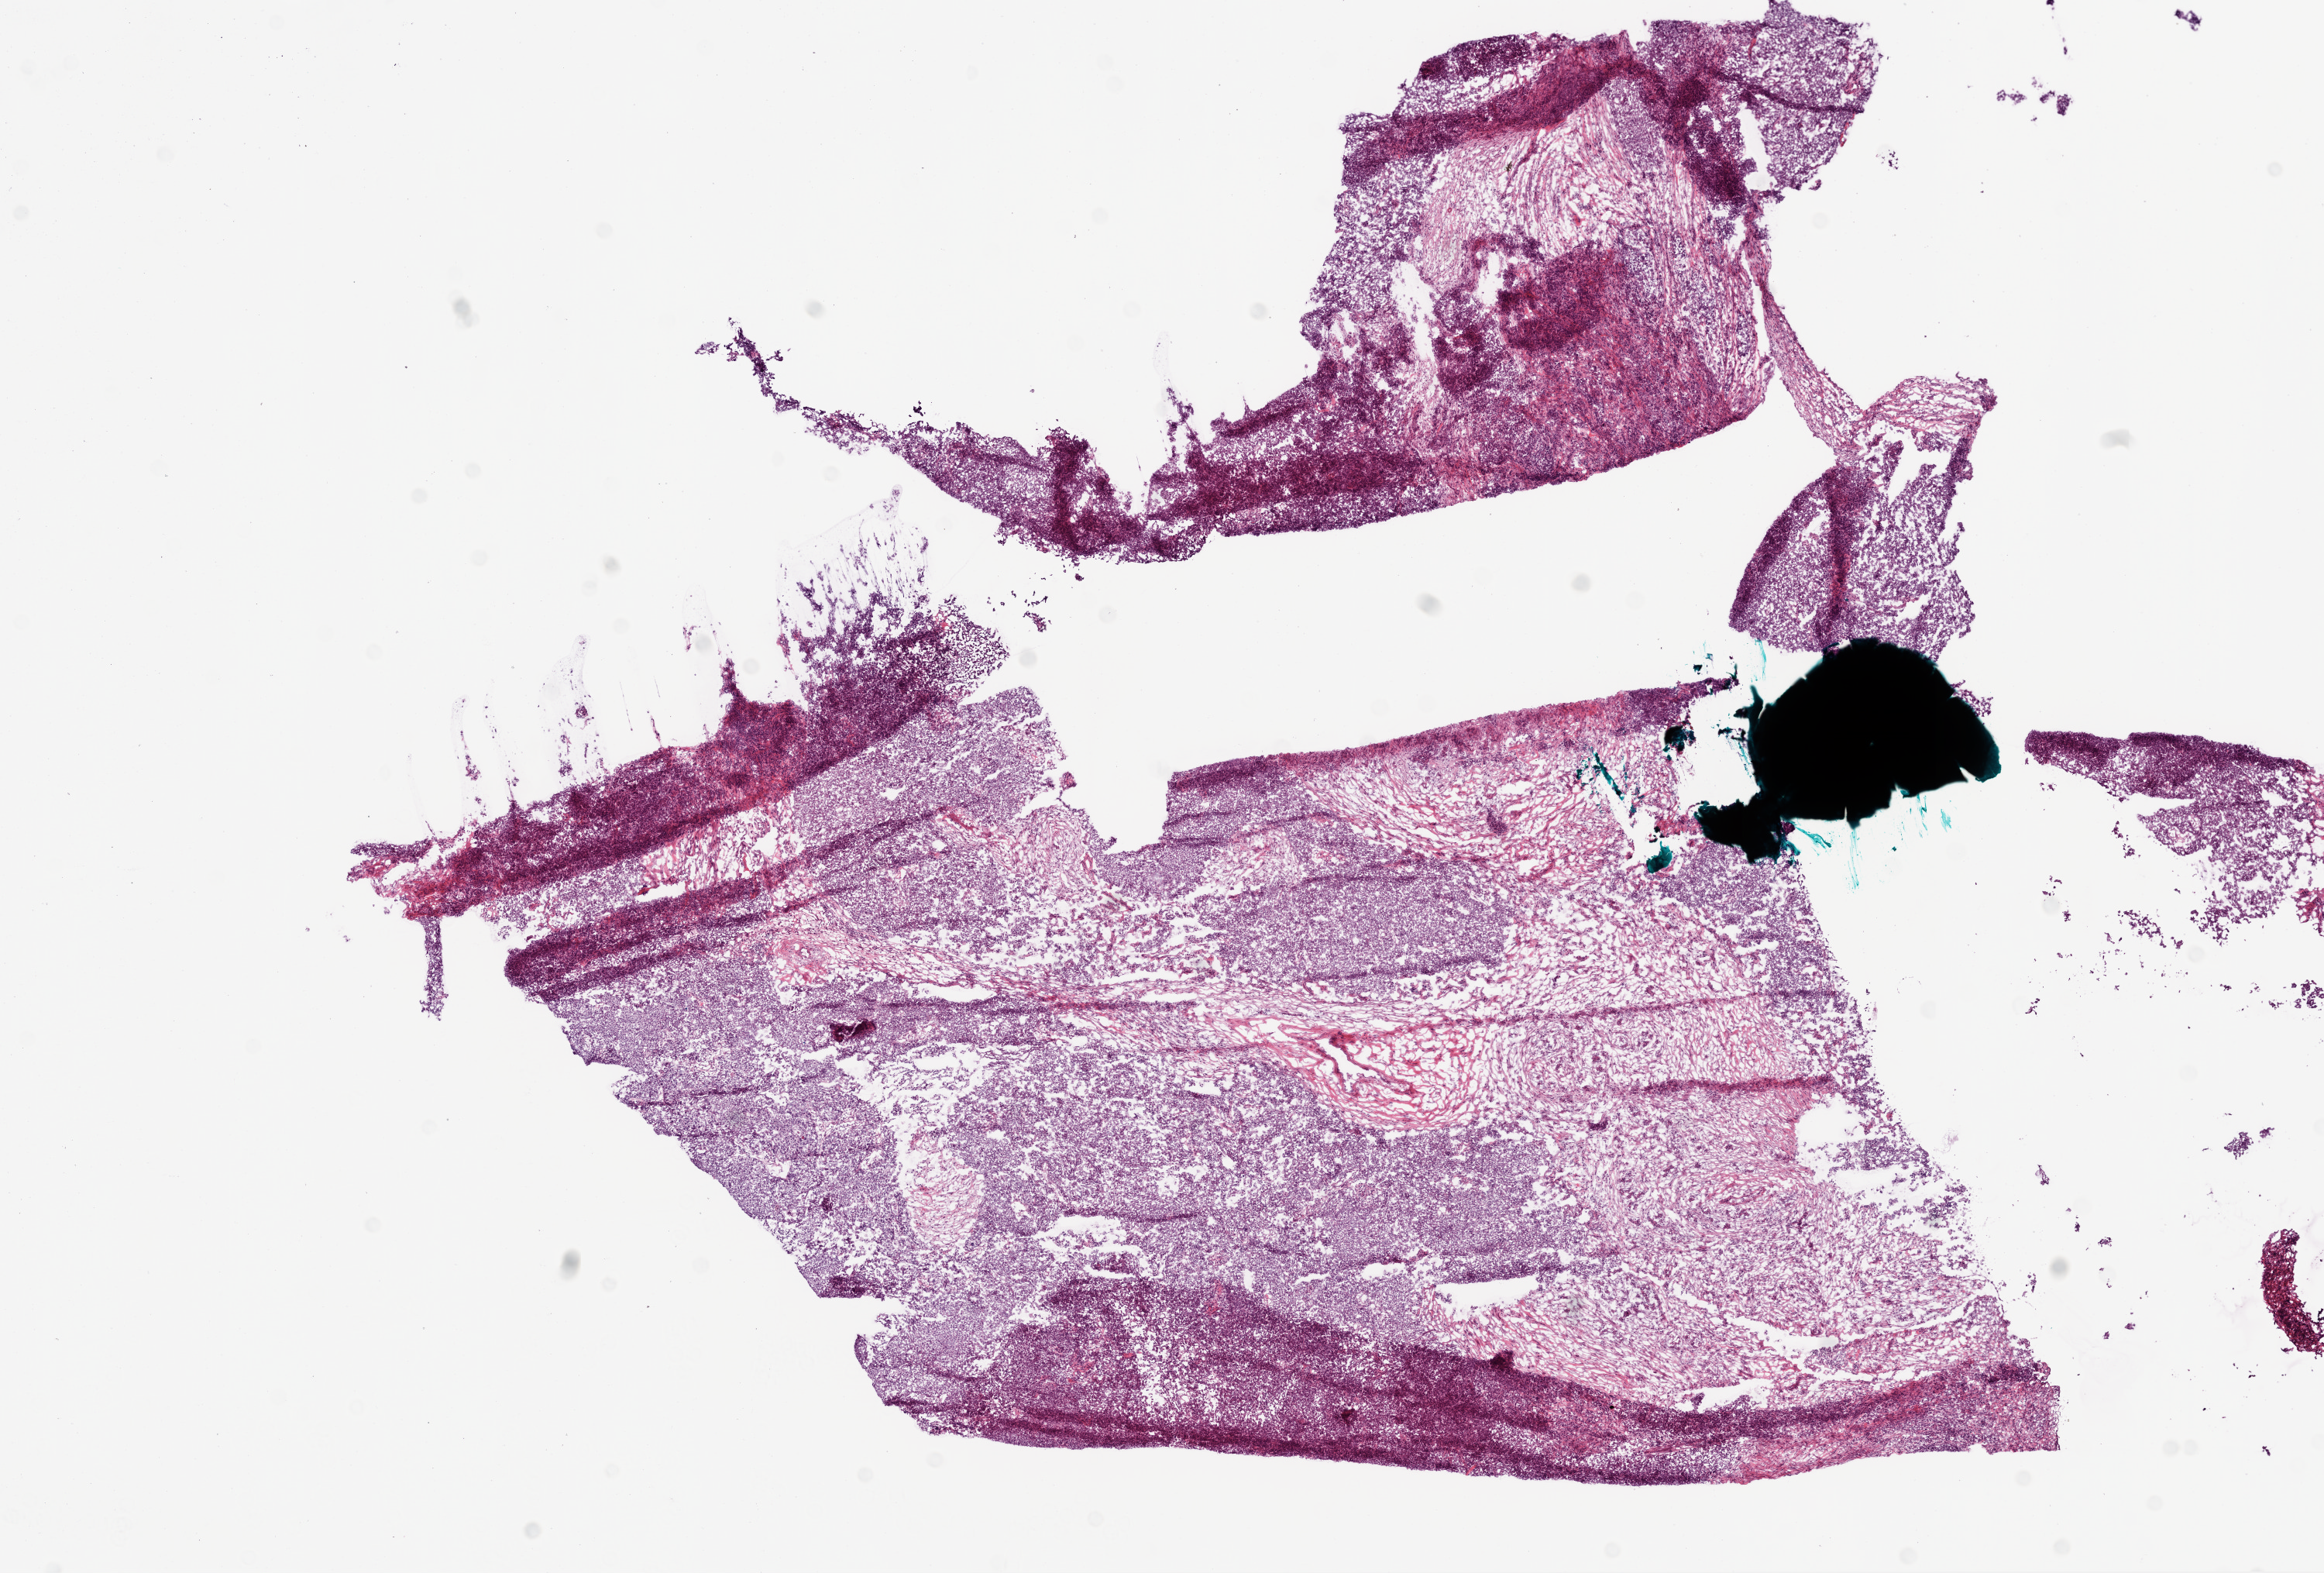
Hematoxylin and eosin (H&E) stained whole-slide image — low-resolution overview of the scanned area, about 12.0 x 8.1 mm, frozen section, primary tumour sample from the ovary. Female patient; age at initial diagnosis 54 years. Histologic grade: G3 (poorly differentiated). Composition of this section per pathologist review: tumour cells 70%, tumour nuclei 70%, normal cells 0%, stromal cells 29%, necrosis 1%.
FIGO stage: IIIB. Laterality: bilateral. Histologic diagnosis: Serous cystadenocarcinoma, NOS.